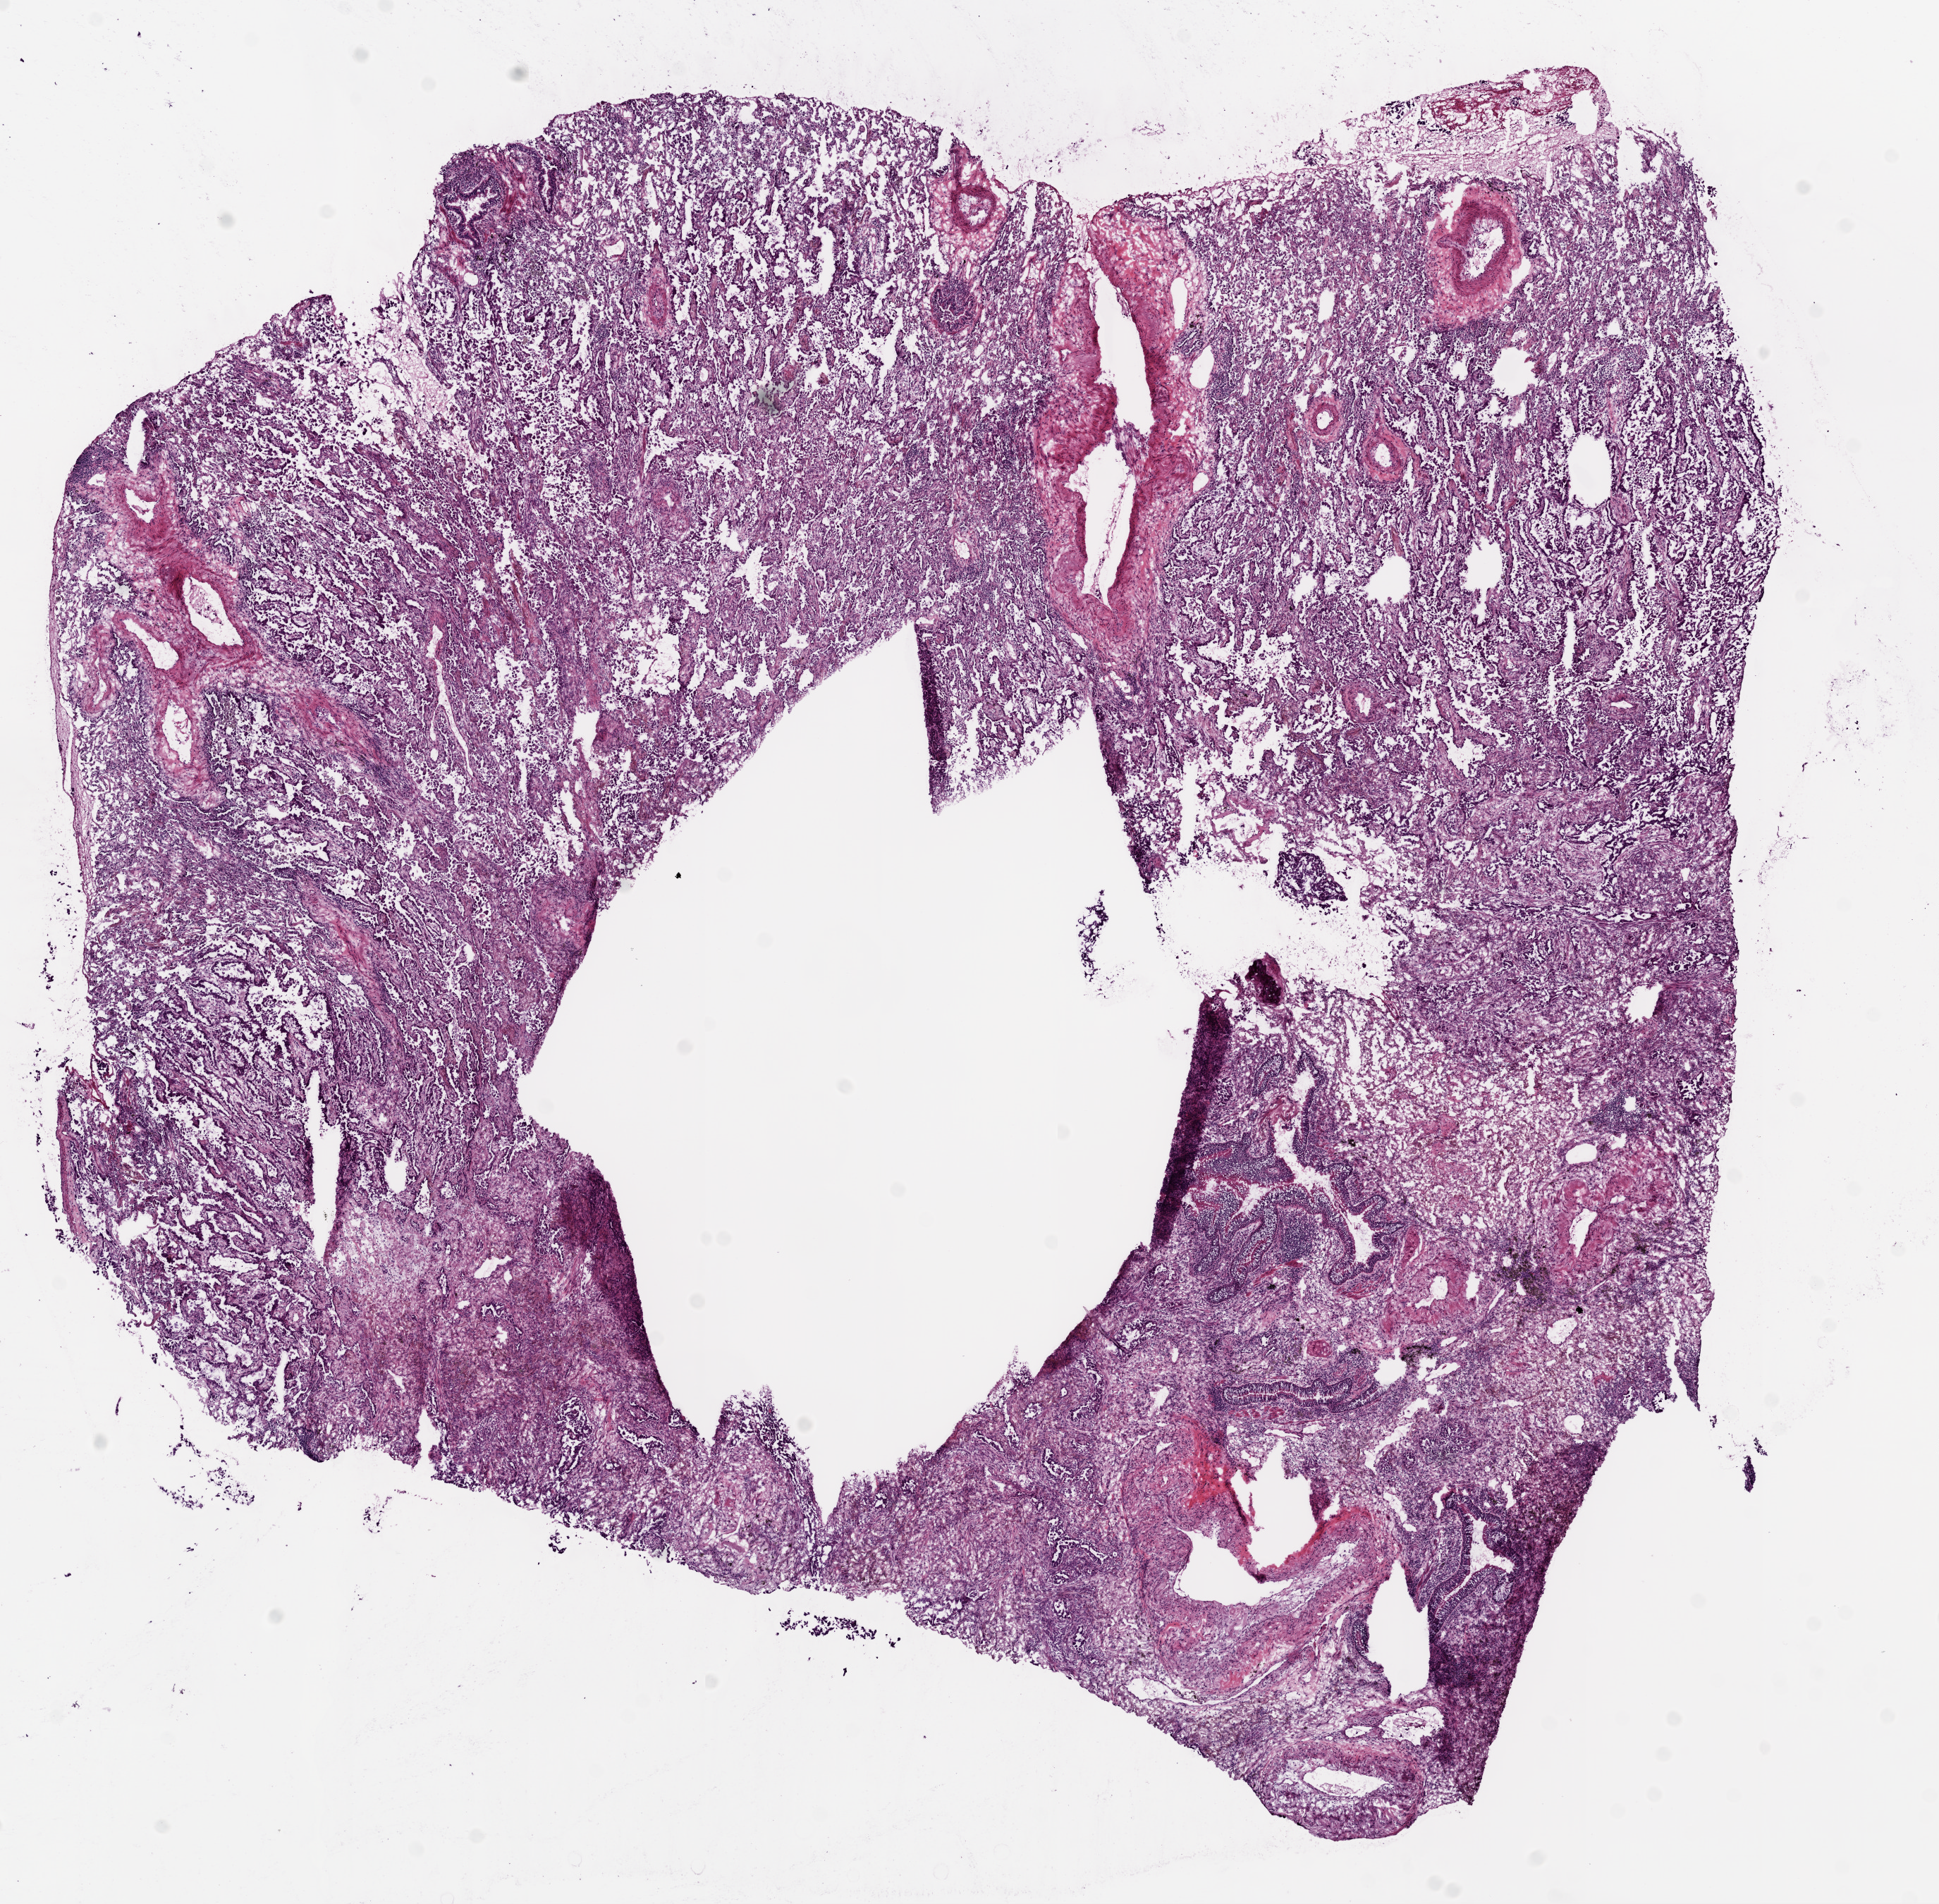
Digitized Hematoxylin and eosin (H&E) stained tissue section (whole slide) — low-resolution overview of the scanned area, about 11.0 x 10.8 mm. Frozen section from the bottom of the tissue portion. Primary tumour sample from the lung. Patient: female, age at initial diagnosis 59 years. Composition of this section per pathologist review: tumour cells 70%, tumour nuclei 75%, normal cells 10%, stromal cells 20%, necrosis 0%.
* laterality: left
* diagnosis: Adenocarcinoma with mixed subtypes
* AJCC pathologic stage: IB (6th edition)
* TNM: T2 N0 M0